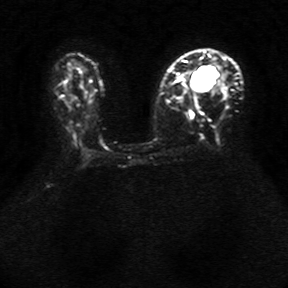
Breast MRI, one axial slice. Position 18 of 34 along the scan axis. Diffusion-weighted series; image 2 of 4 stored at this slice position (different b-values; order by instance number). 1.5 T. 5 mm slice thickness. 288 × 288 image matrix, field of view 340 × 340 mm. Female patient.
Annotated regions visible in this slice (outlined manually by an expert reader):
- tumour on diffusion-weighted imaging: box from (x=191, y=73) to (x=215, y=89) px